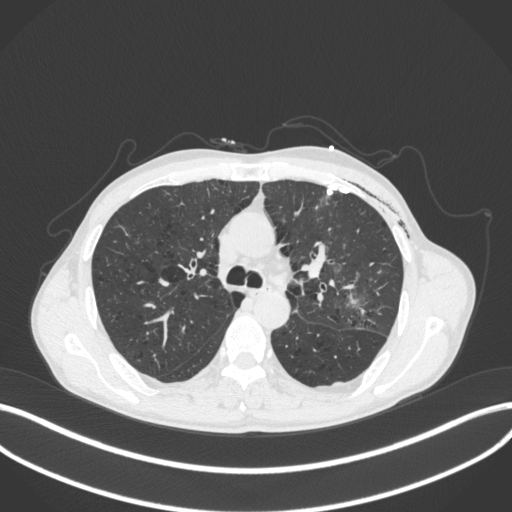
Chest CT, one axial slice; position 264 of 416 along the scan axis; reconstruction kernel B31f; 120 kVp; lung window (W 1500 / L -600 HU); 1 mm slice thickness; 512 × 512 image matrix, field of view 400 × 400 mm. Male patient, age 58 years. From the clinical record (not read from this slice): clinical TNM (as recorded): T3 N0 M0.
Annotated regions visible in this slice (rectangle marked by the reading radiologist):
- lung tumour (recorded histology: adenocarcinoma): bounding box (x1, y1, x2, y2) in pixels: (344, 274, 369, 310)